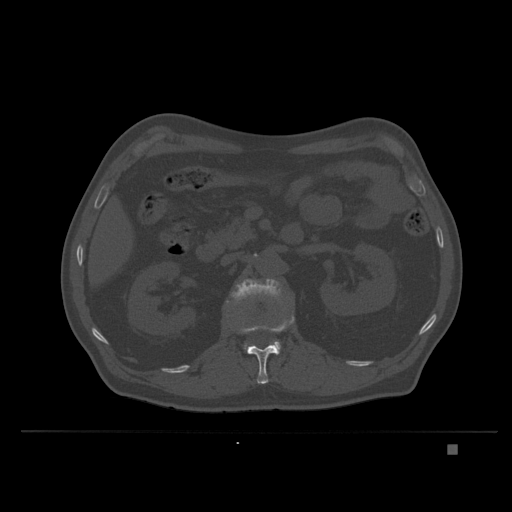
CT including the spine, one axial slice; position 131 of 435 along the scan axis; bone window (W 1800 / L 400 HU); 512 × 512 image matrix. Male patient, age 73 years. Case-level facts recorded for this patient, not image findings: primary cancer: skin.
Annotated regions visible in this slice (semi-automatically segmented with operator editing):
- L1 vertebra: bounding box [x1, y1, x2, y2] px = [229, 311, 295, 384]
- L2 vertebra: [231, 278, 283, 353]